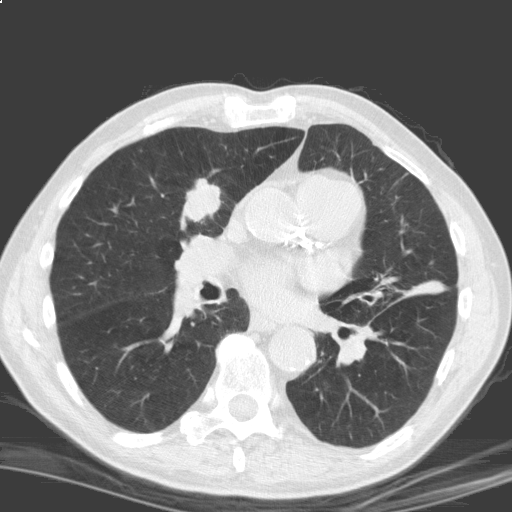
Low-dose screening chest CT, axial slice, second annual screen, lung window (W 1500 / L -600 HU), 3.2 mm slice thickness, standard (soft-tissue) reconstruction kernel (C), 512 × 512 image matrix, field of view 329 × 329 mm. Male, age 69 years at enrolment. Current smoker at enrolment.
Expert-annotated lung lesion, bounding box (x1, y1, x2, y2) in pixels: (170, 168, 231, 227). The screening reader recorded 2 non-calcified nodules or masses ≥4 mm on this exam (right upper lobe, left lower lobe); which of them this box marks is not recorded. Official screen result: positive, other. Later outcome: lung cancer diagnosed 17 days after this screen — squamous cell carcinoma, NOS, right upper lobe, moderately differentiated (G2), stage IB (AJCC 6th edition), 40 mm at pathology.